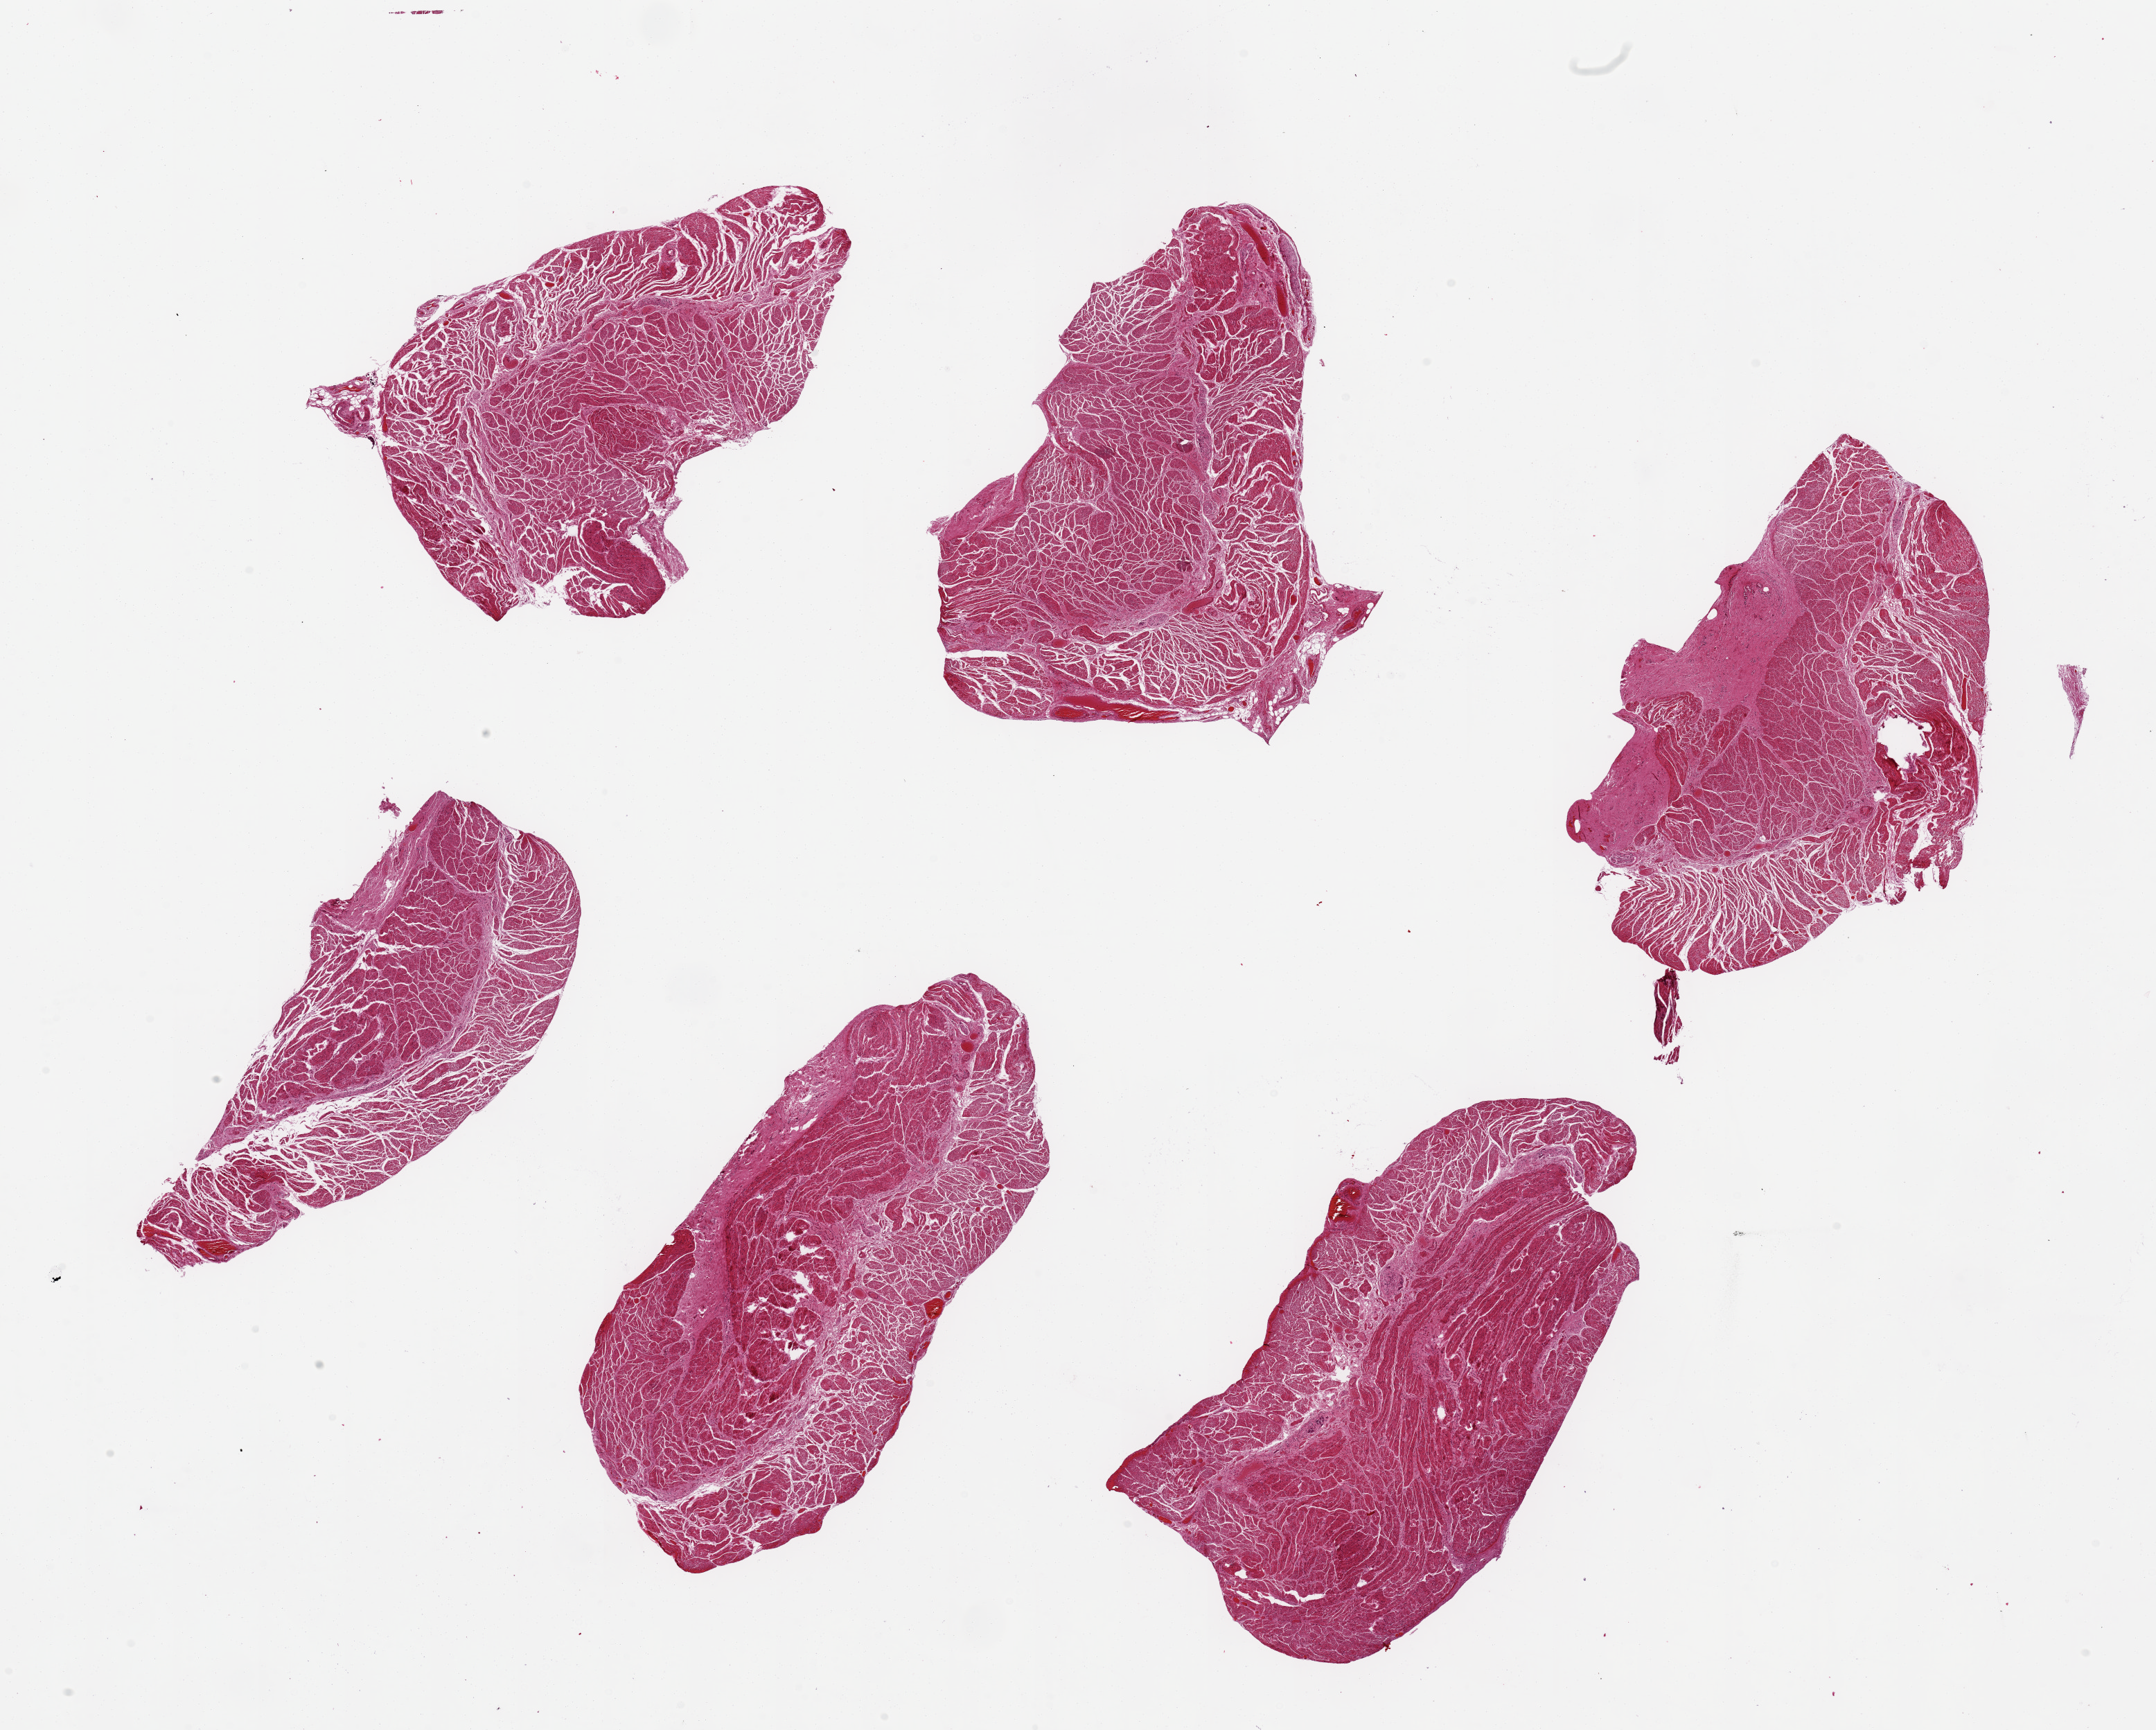
Digitized H&E-stained section — shown as a low-resolution overview of the whole scanned area (about 24.6 x 19.7 mm, slide scanned at 20x); PAXgene-fixed paraffin-embedded (PFPE) section; sampled site (target tissue): esophageal muscle; tissue donor sample. Donor sex: male.
Review note (as recorded): 6 pieces ~6x3mm.